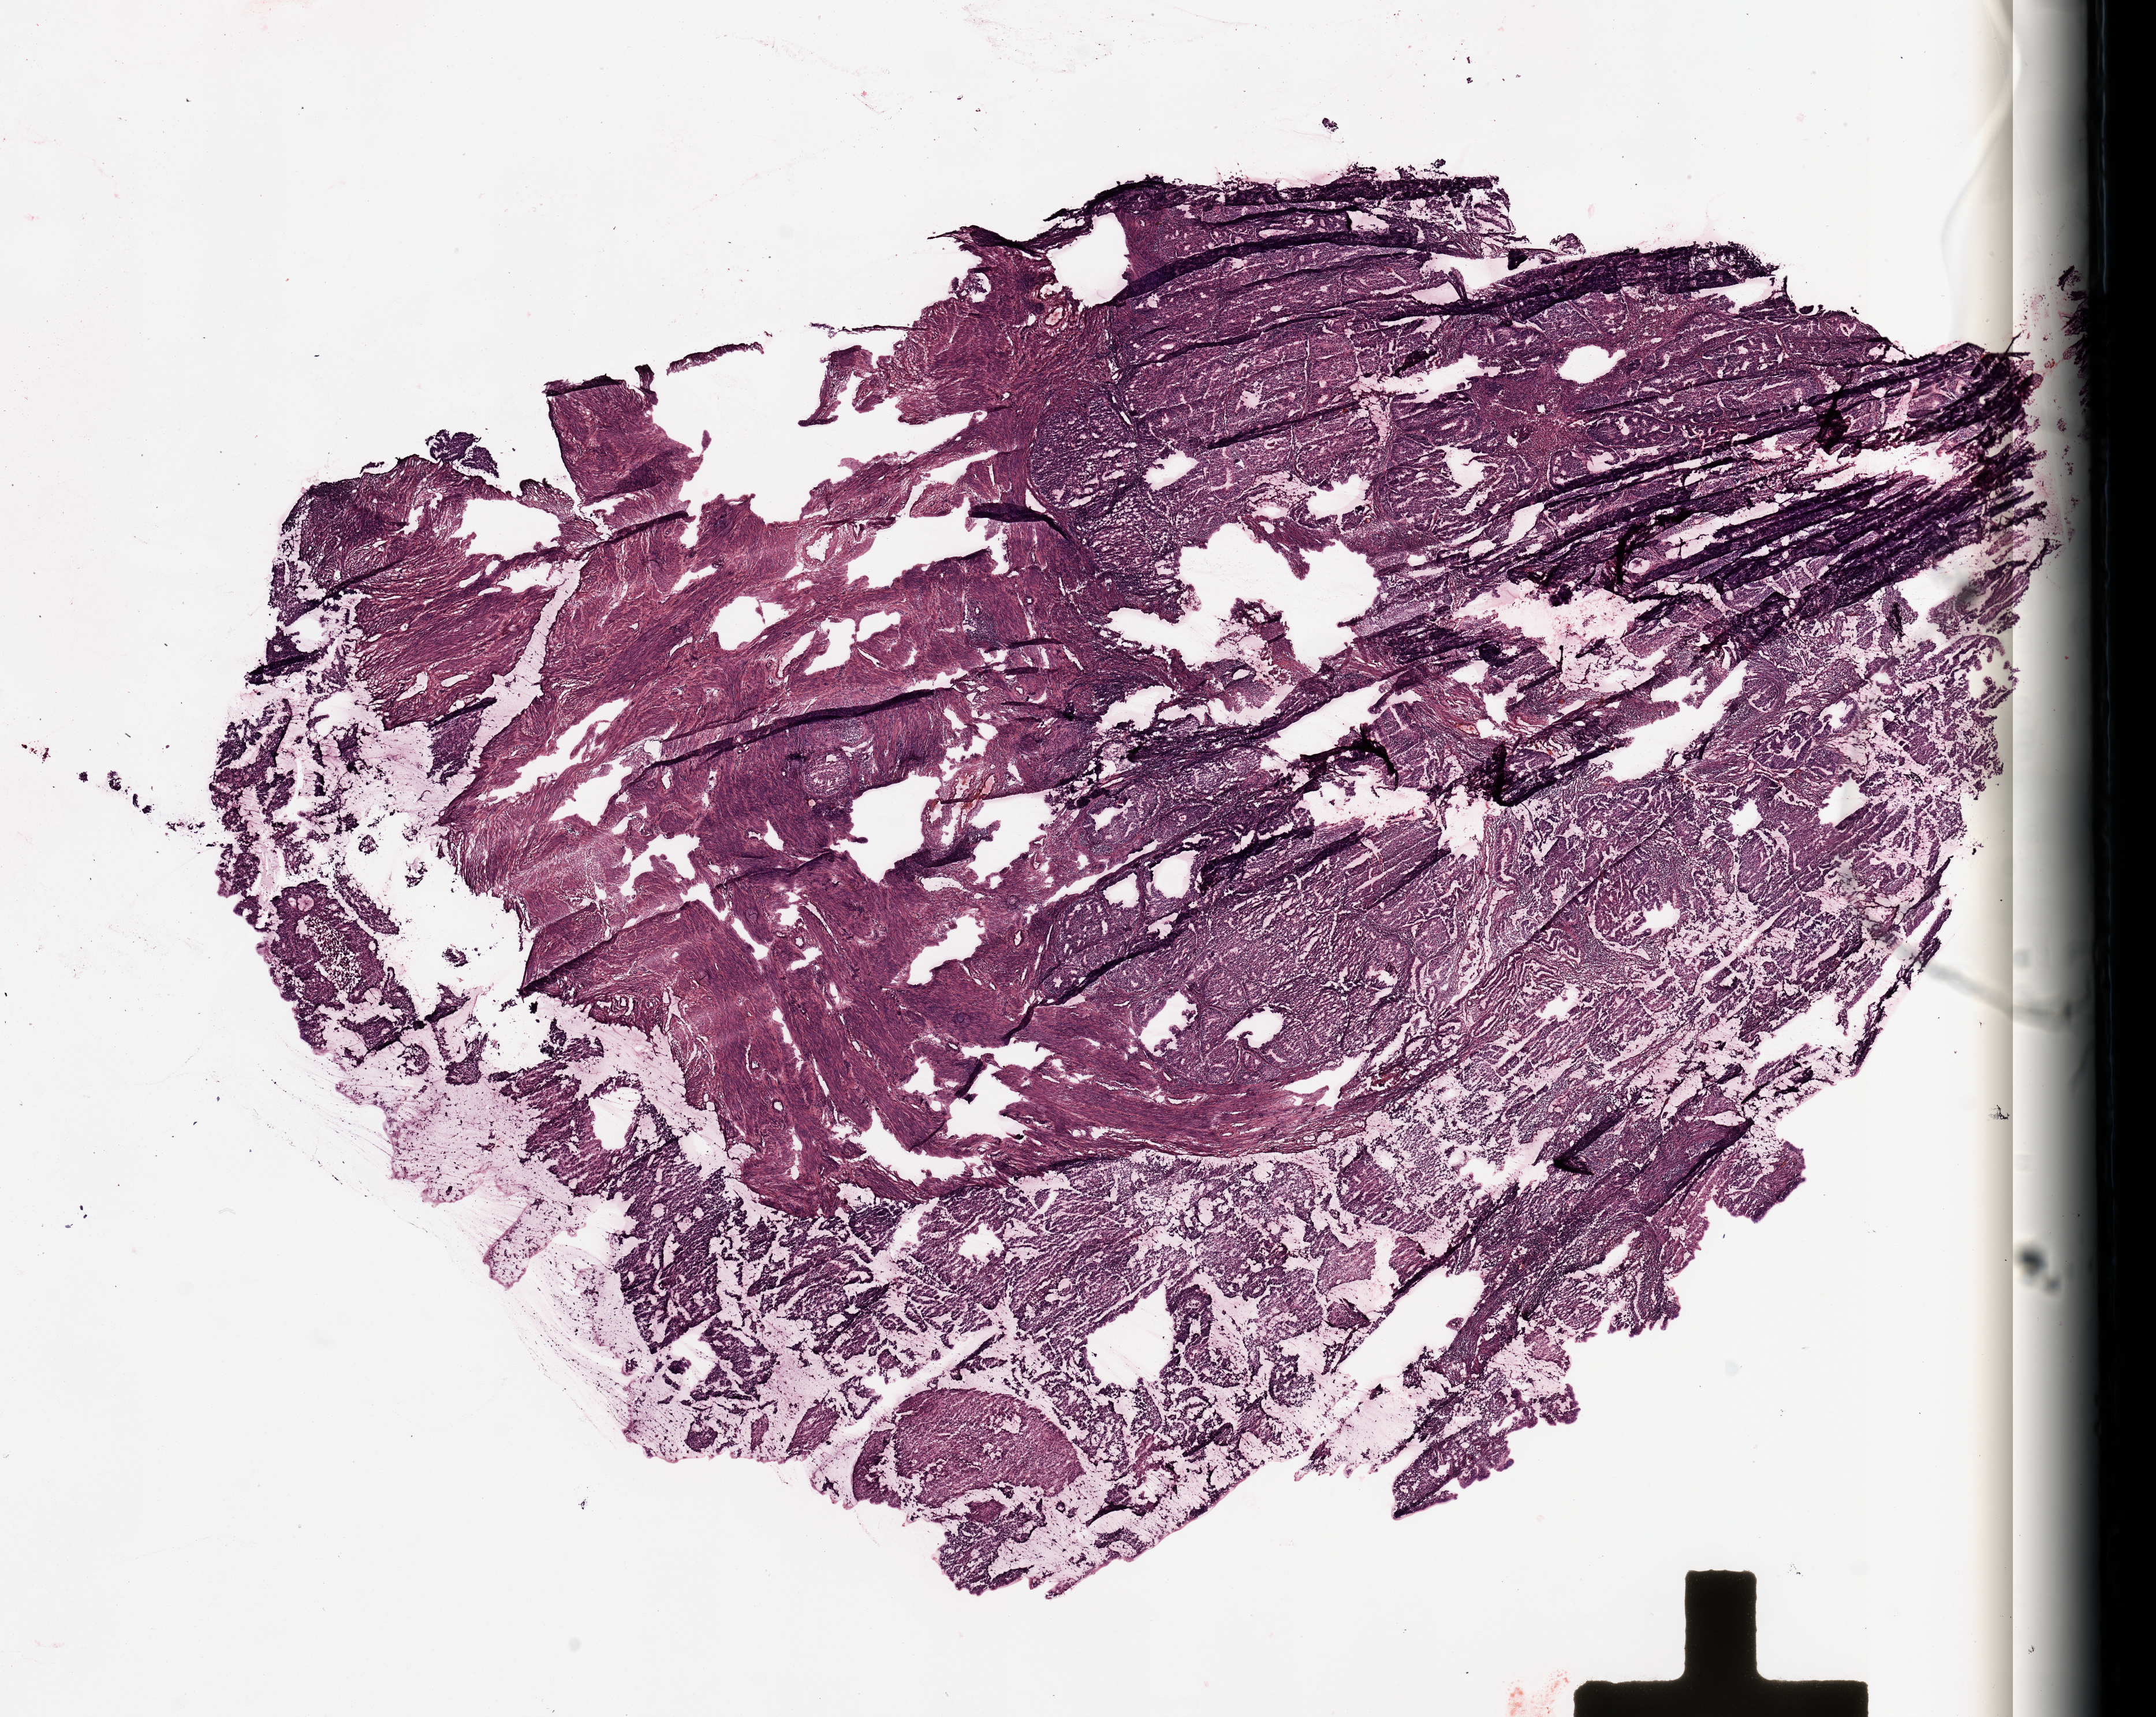
Digitized Hematoxylin and eosin (H&E) stained tissue section (whole slide), whole scanned area (about 14.8 x 11.8 mm) shown as a low-resolution overview, uterus, tumour tissue. Female, 45 y/o. Histologic grade: G2 (moderately differentiated).
Diagnosis: Endometrioid adenocarcinoma, NOS. AJCC pathologic stage: I.